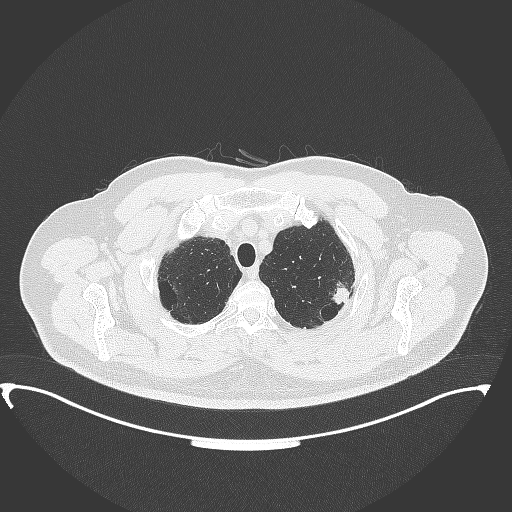
Chest CT, one axial slice; slice 319 of 350 in the series (ordered by position); reconstruction kernel B70f; lung window (W 1500 / L -600 HU); 1 mm slice thickness; 512 × 512 image matrix, field of view 459 × 459 mm. Patient: male, 64 years. Case-level facts recorded for this patient, not image findings: clinical TNM (as recorded): T1c N1 M1.
Structures marked on this image (bounding box drawn by a radiologist):
- lung tumour (recorded histology: adenocarcinoma): bounding box <328,278,352,307> (left, top, right, bottom; pixels)